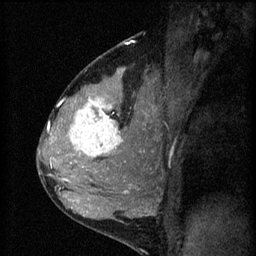
Breast MRI (dynamic contrast-enhanced), one sagittal slice; position 38 of 60 along the scan axis; 3 images stored at this slice position (order not interpretable as contrast timing); 1.5 T; TE 4.2 ms, TR 8.2 ms; 2 mm slice thickness; 256 × 256 image matrix, field of view 180 × 180 mm. Female patient, age 37 years.
Structures marked on this image (semi-automatically segmented with operator editing):
- analysis volume of interest (the breast-tissue region the enhancement analysis was run in; not a lesion): bounding box [x1, y1, x2, y2] px = [53, 78, 140, 181]
- tumour enhancement mask (voxels above the 70 % enhancement threshold inside the analysis volume of interest): [63, 98, 123, 181]